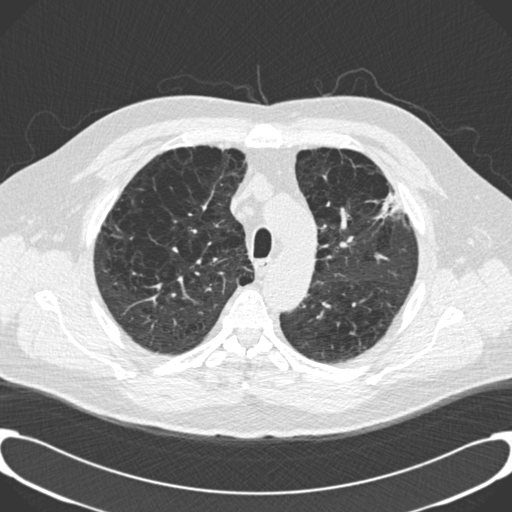
Low-dose screening chest CT, one axial slice; position 150 of 189 along the scan axis; 120 kVp; lung window (W 1500 / L -600 HU); 2 mm slice thickness; 512 × 512 image matrix, field of view 380 × 380 mm.
Annotated regions visible in this slice (manually delineated by an expert):
- lesion 1 (tumor, upper lobe of left lung): box from (x=376, y=192) to (x=405, y=219) px